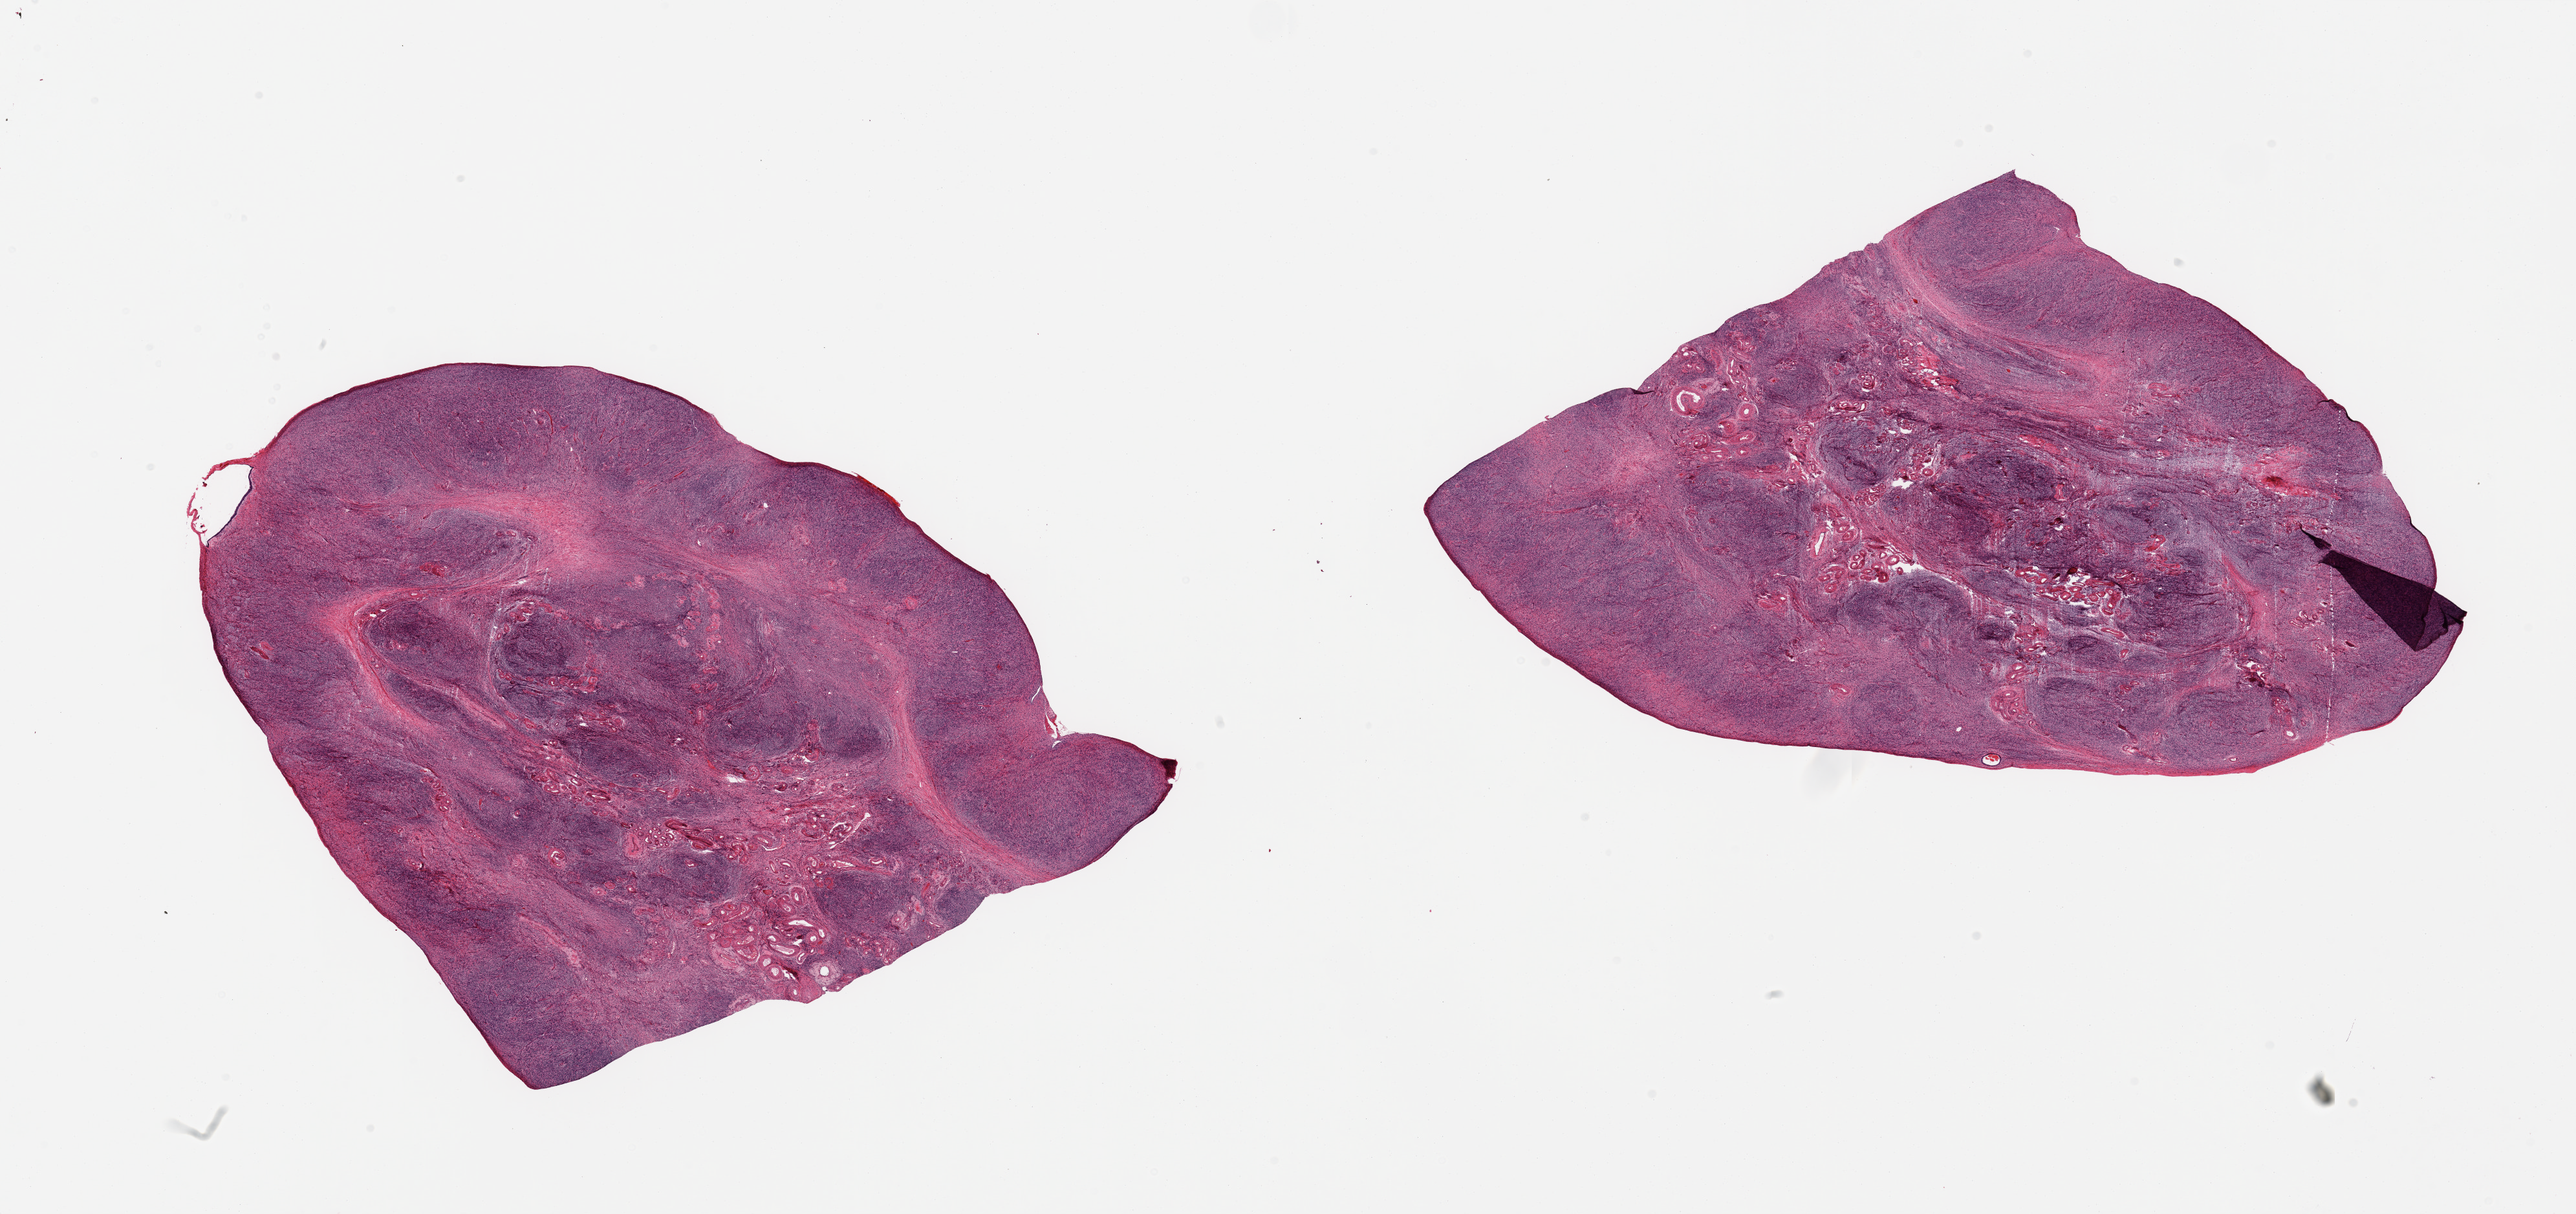
Whole-slide image, H&E stain — shown as a low-resolution overview of the whole scanned area (about 31.5 x 14.8 mm, from a 20x scan); PAXgene-fixed paraffin-embedded (PFPE) section; section of ovary (target tissue); donor tissue sample. Donor: female.
Reviewer comment on this tissue sample: 2 pieces; 1 mm epithelial cyst.